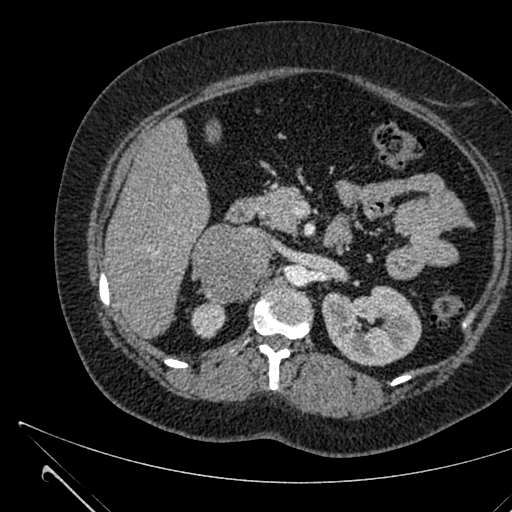
Contrast-enhanced abdominal CT, one axial slice; slice 384 of 731 in the series (ordered by position); intravenous contrast given; soft-tissue window (W 400 / L 40 HU); 1 mm slice thickness; 512 × 512 image matrix, field of view 376 × 376 mm. Patient: female, 36 years. From the clinical record (not read from this slice): diagnosis: adrenocortical carcinoma; tumour side: right adrenal; tumour size at pathology: 10 cm; Ki-67 index: 20 %; stage (as recorded): 4.
Annotated regions visible in this slice (semi-automatically segmented with operator editing):
- mass: bounding box [x1, y1, x2, y2] px = [193, 224, 272, 302]